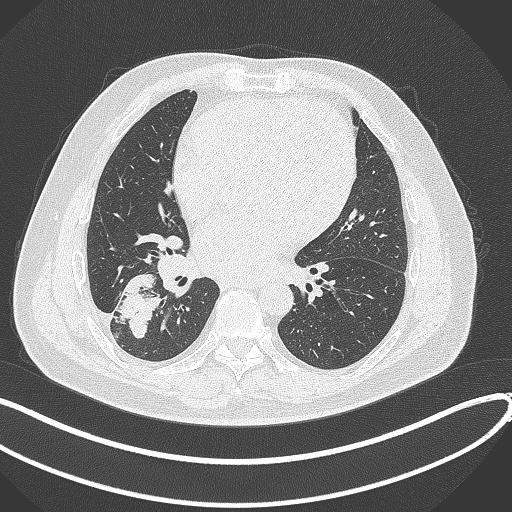
Chest CT, one axial slice; position 161 of 360 along the scan axis; reconstruction kernel B70f; 120 kVp; lung window (W 1500 / L -600 HU); 1 mm slice thickness; 512 × 512 image matrix. Male patient, age 59 years.
Annotated regions visible in this slice (rectangle marked by the reading radiologist):
- lung tumour (recorded histology: adenocarcinoma): bounding box (x1, y1, x2, y2) in pixels: (114, 273, 166, 339)